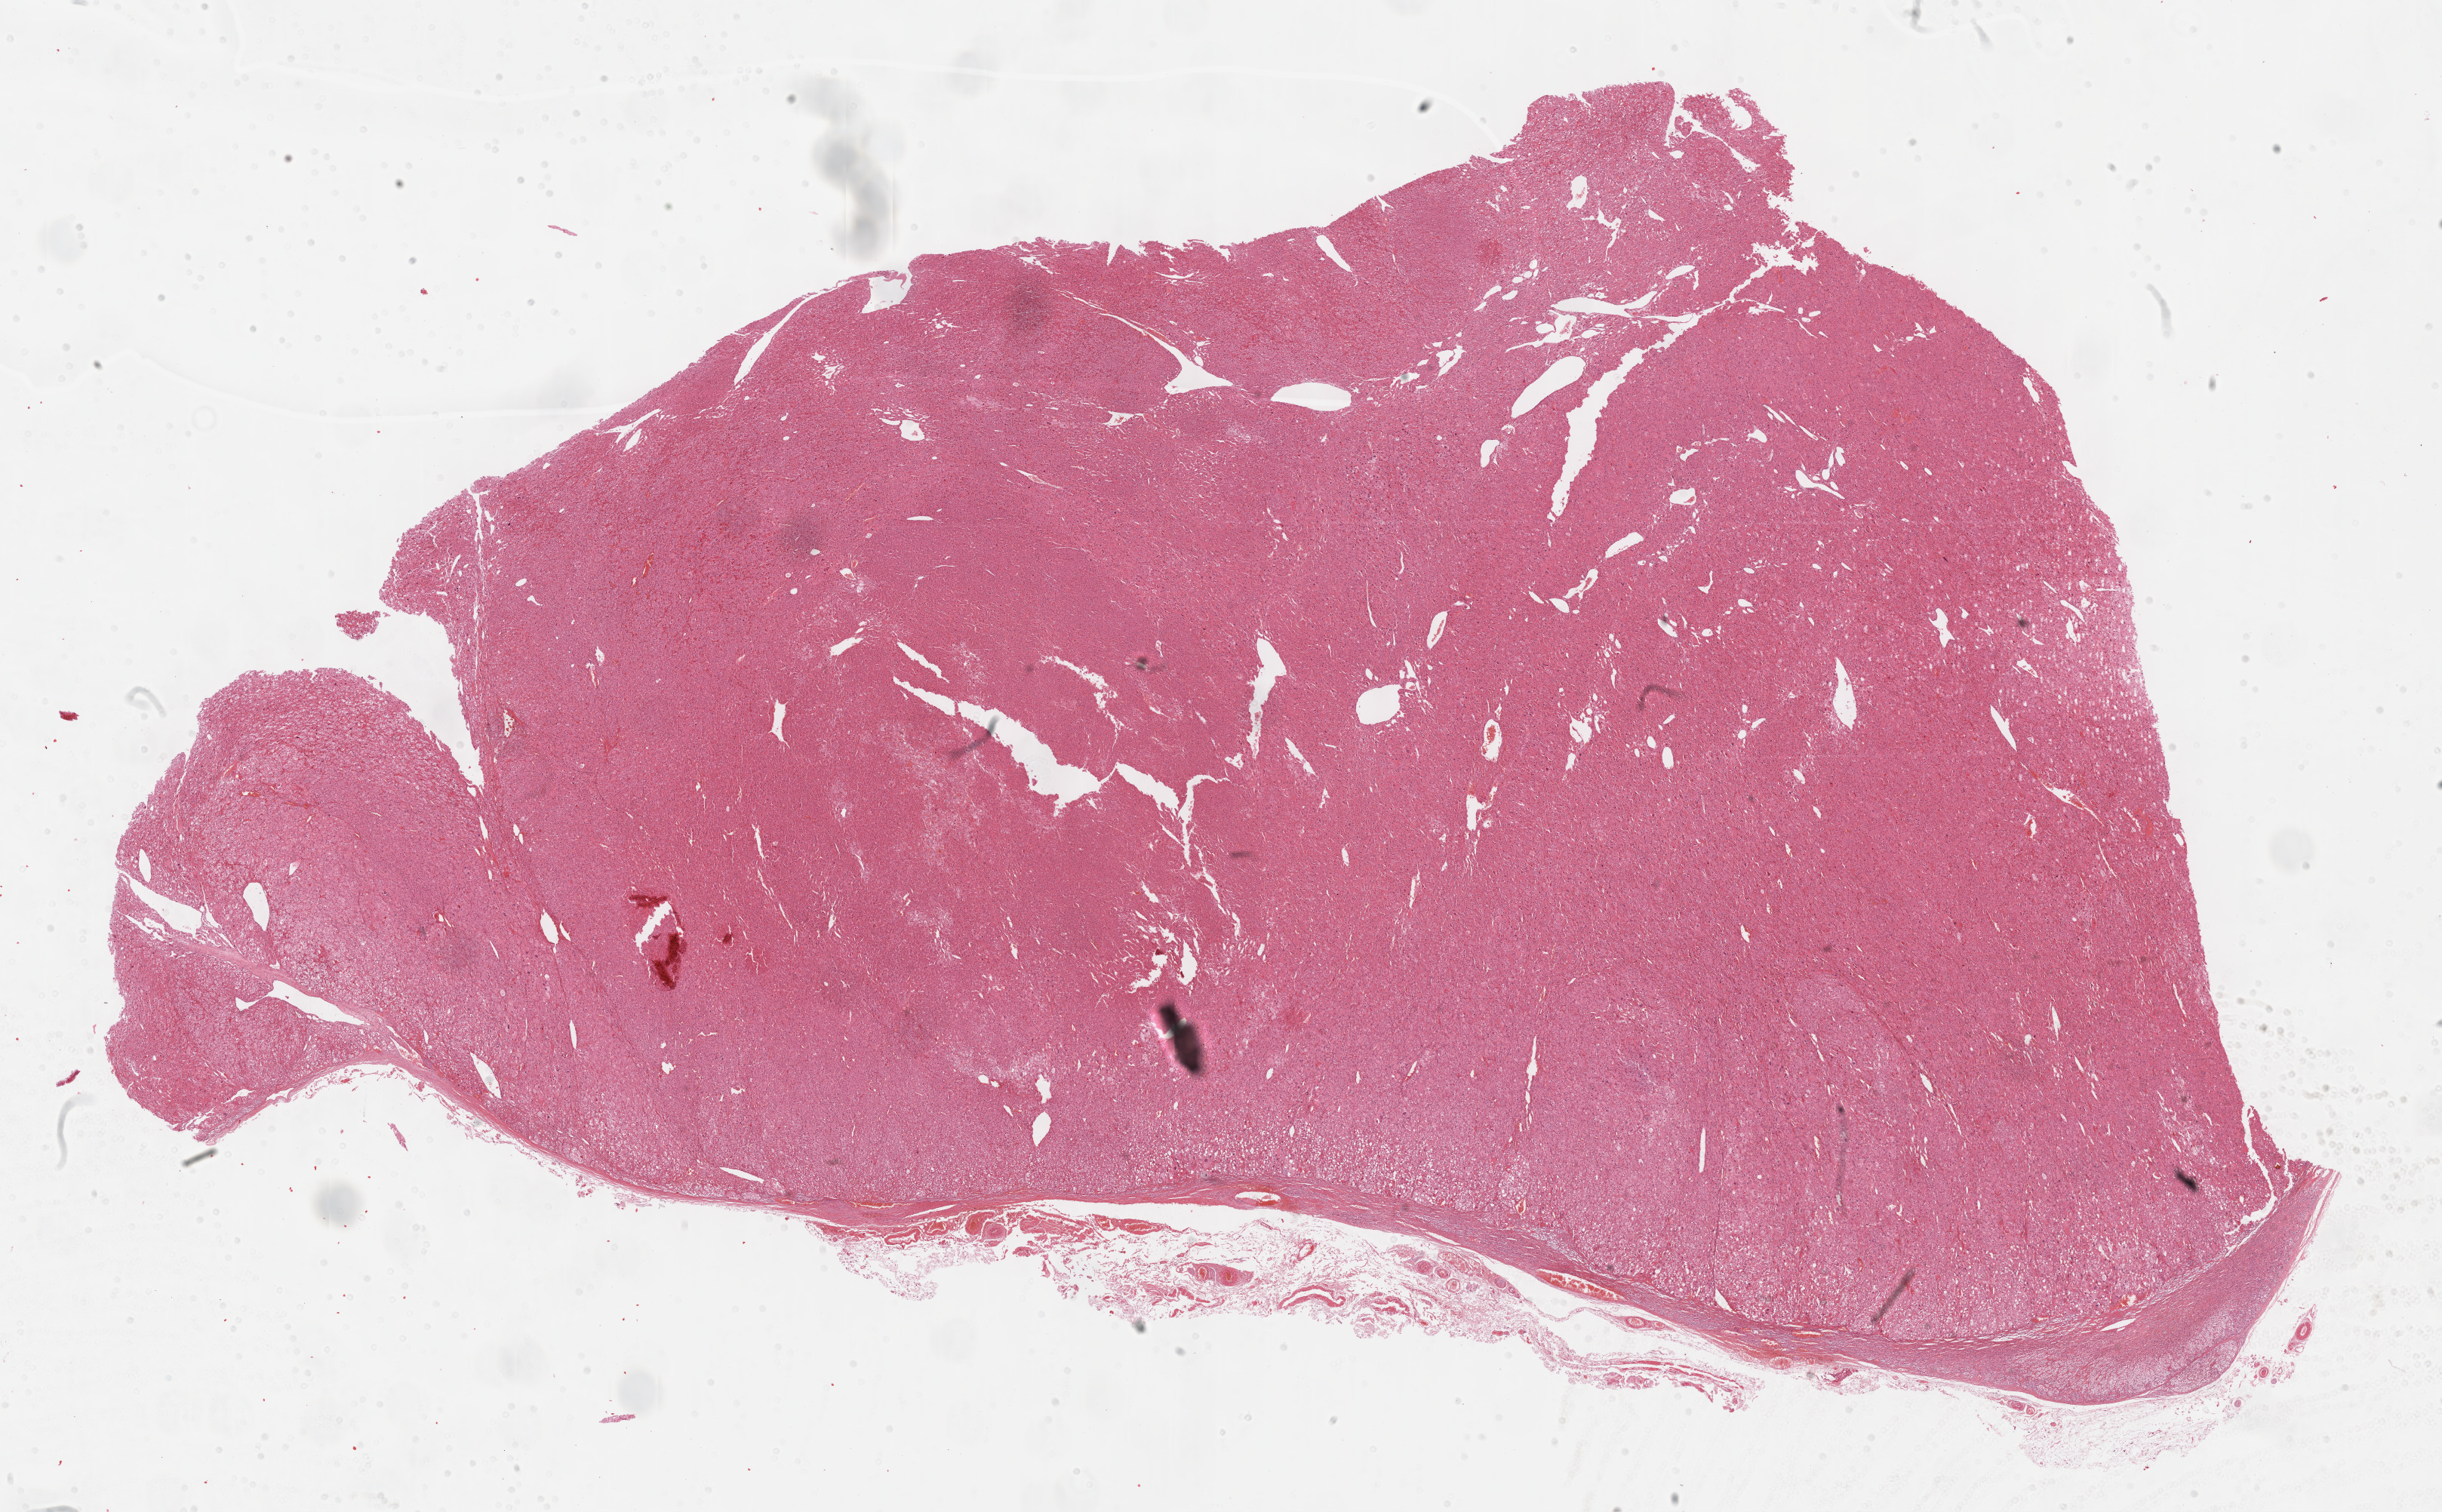
Hematoxylin and eosin (H&E) stained whole-slide image, whole scanned area (about 26.2 x 16.2 mm, slide scanned at 40x) shown as a low-resolution overview, FFPE section, adrenal cortex, primary tumour sample. Patient: female, age at initial diagnosis 36 years.
Diagnosis: Adrenal cortical carcinoma (cortex of adrenal gland).